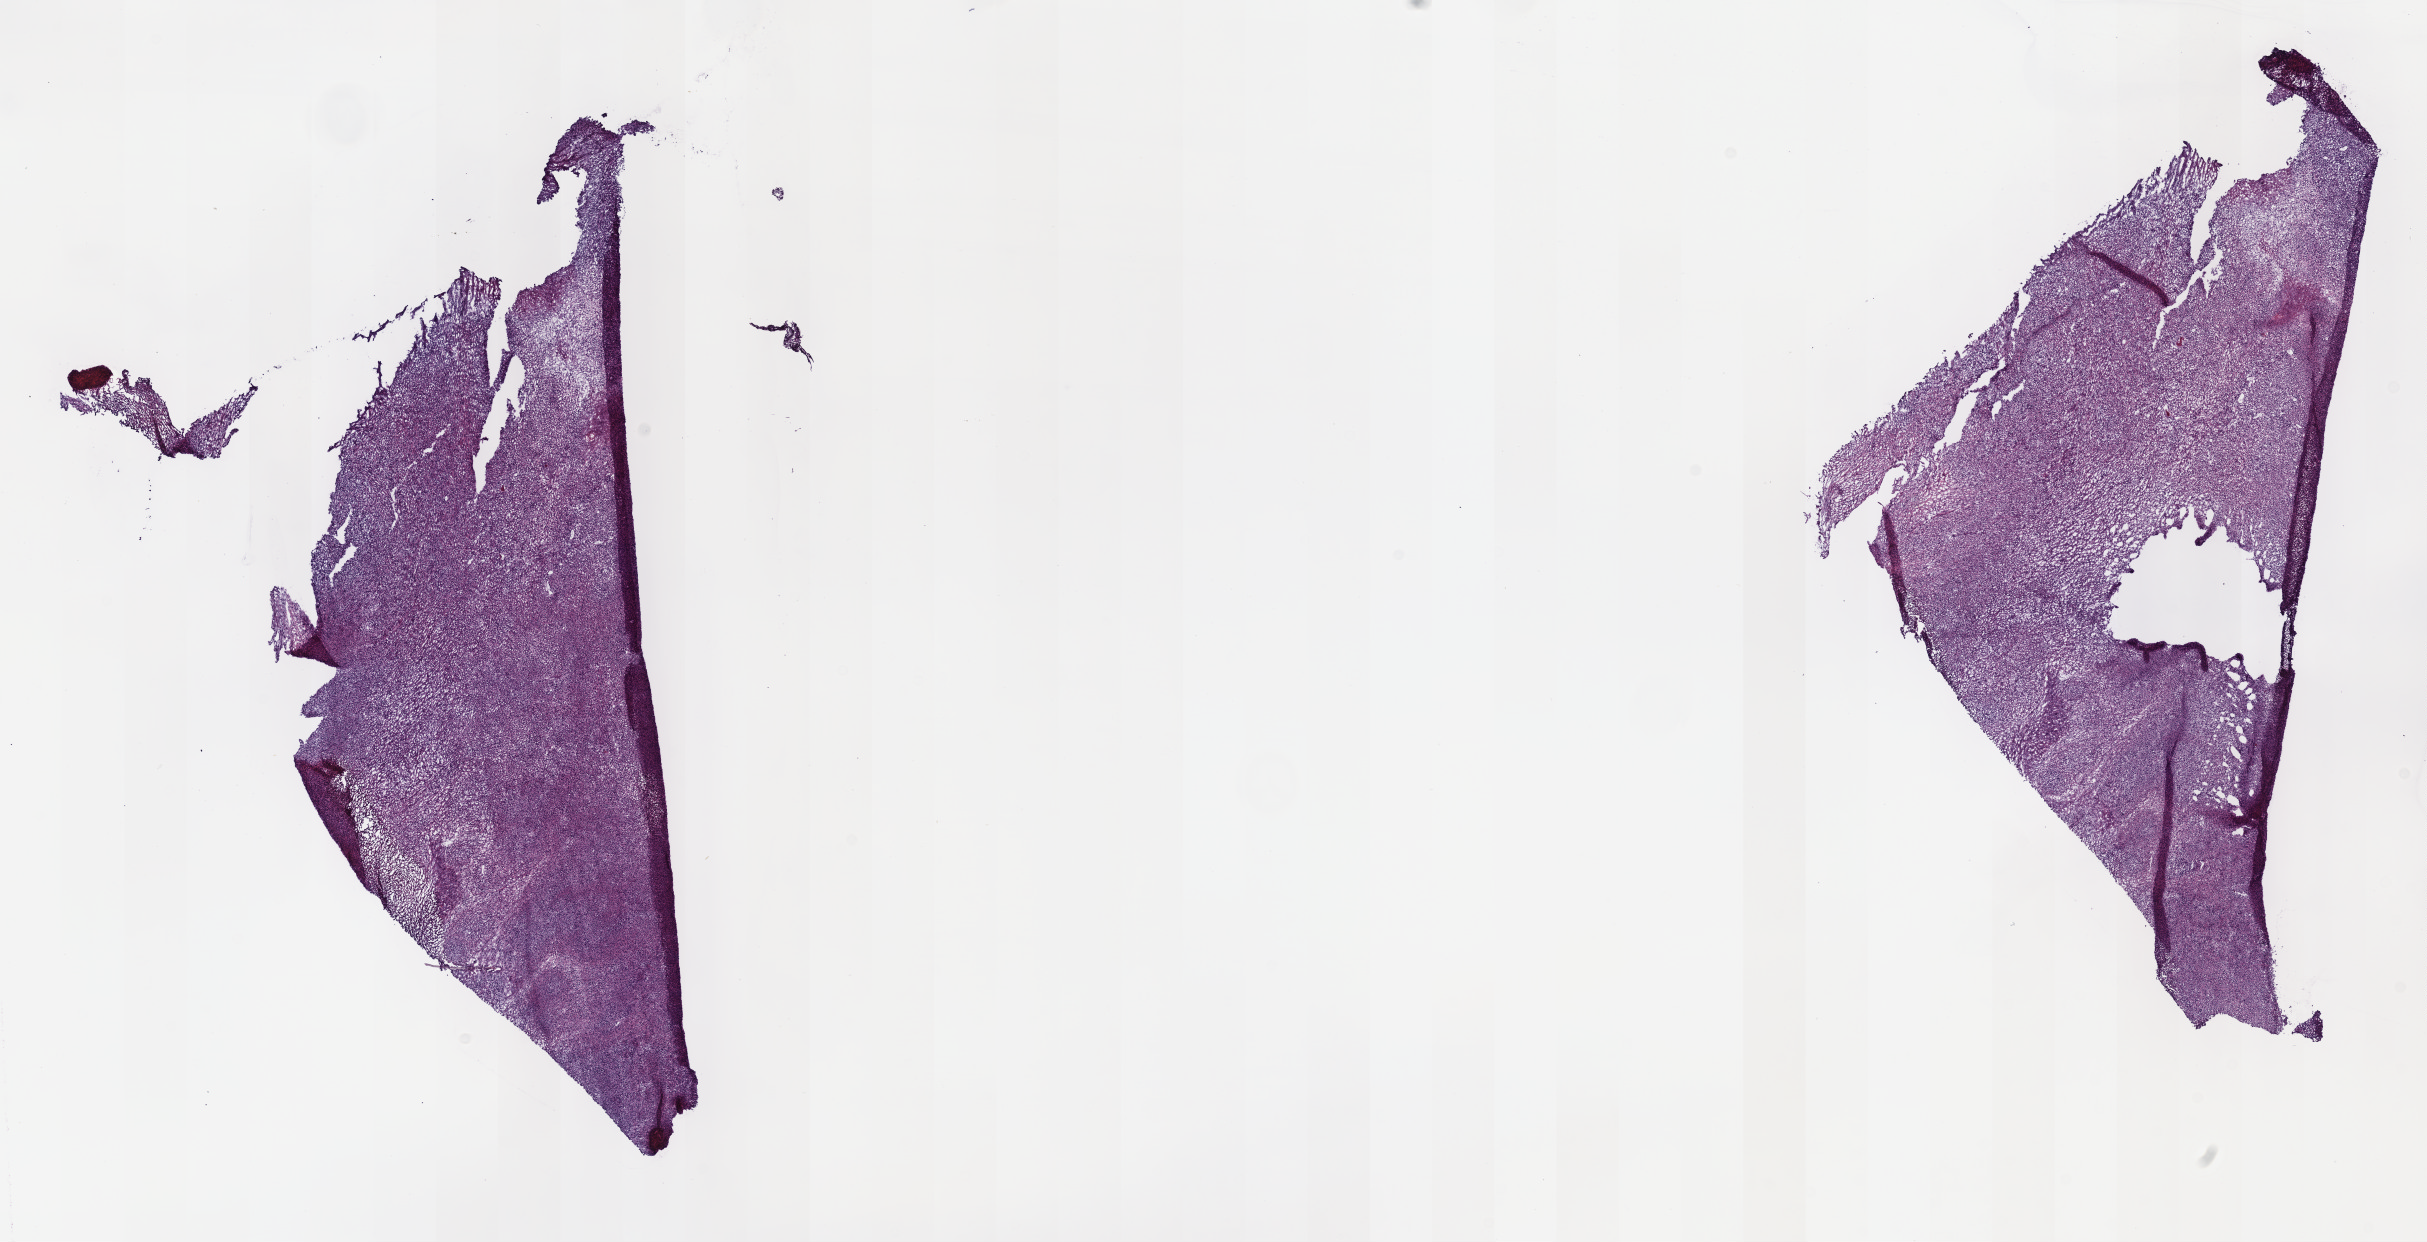
Whole-slide histology image, Hematoxylin and eosin (H&E) stained, shown as a low-resolution overview of the whole scanned area (about 19.6 x 10.0 mm, acquisition: 40x scan), frozen section from the top of the tissue portion, primary tumour sample from the retroperitoneum and peritoneum. Male, age 55 years at initial diagnosis. Slide review estimates, as recorded: tumour cells 80%, tumour nuclei 100%, normal cells 0%, stromal cells 20%, necrosis 0%. Infiltration values recorded for this section: lymphocyte infiltration 0%, monocyte infiltration 0%, neutrophil infiltration 0%.
Pathologic diagnosis: Undifferentiated sarcoma (retroperitoneum).